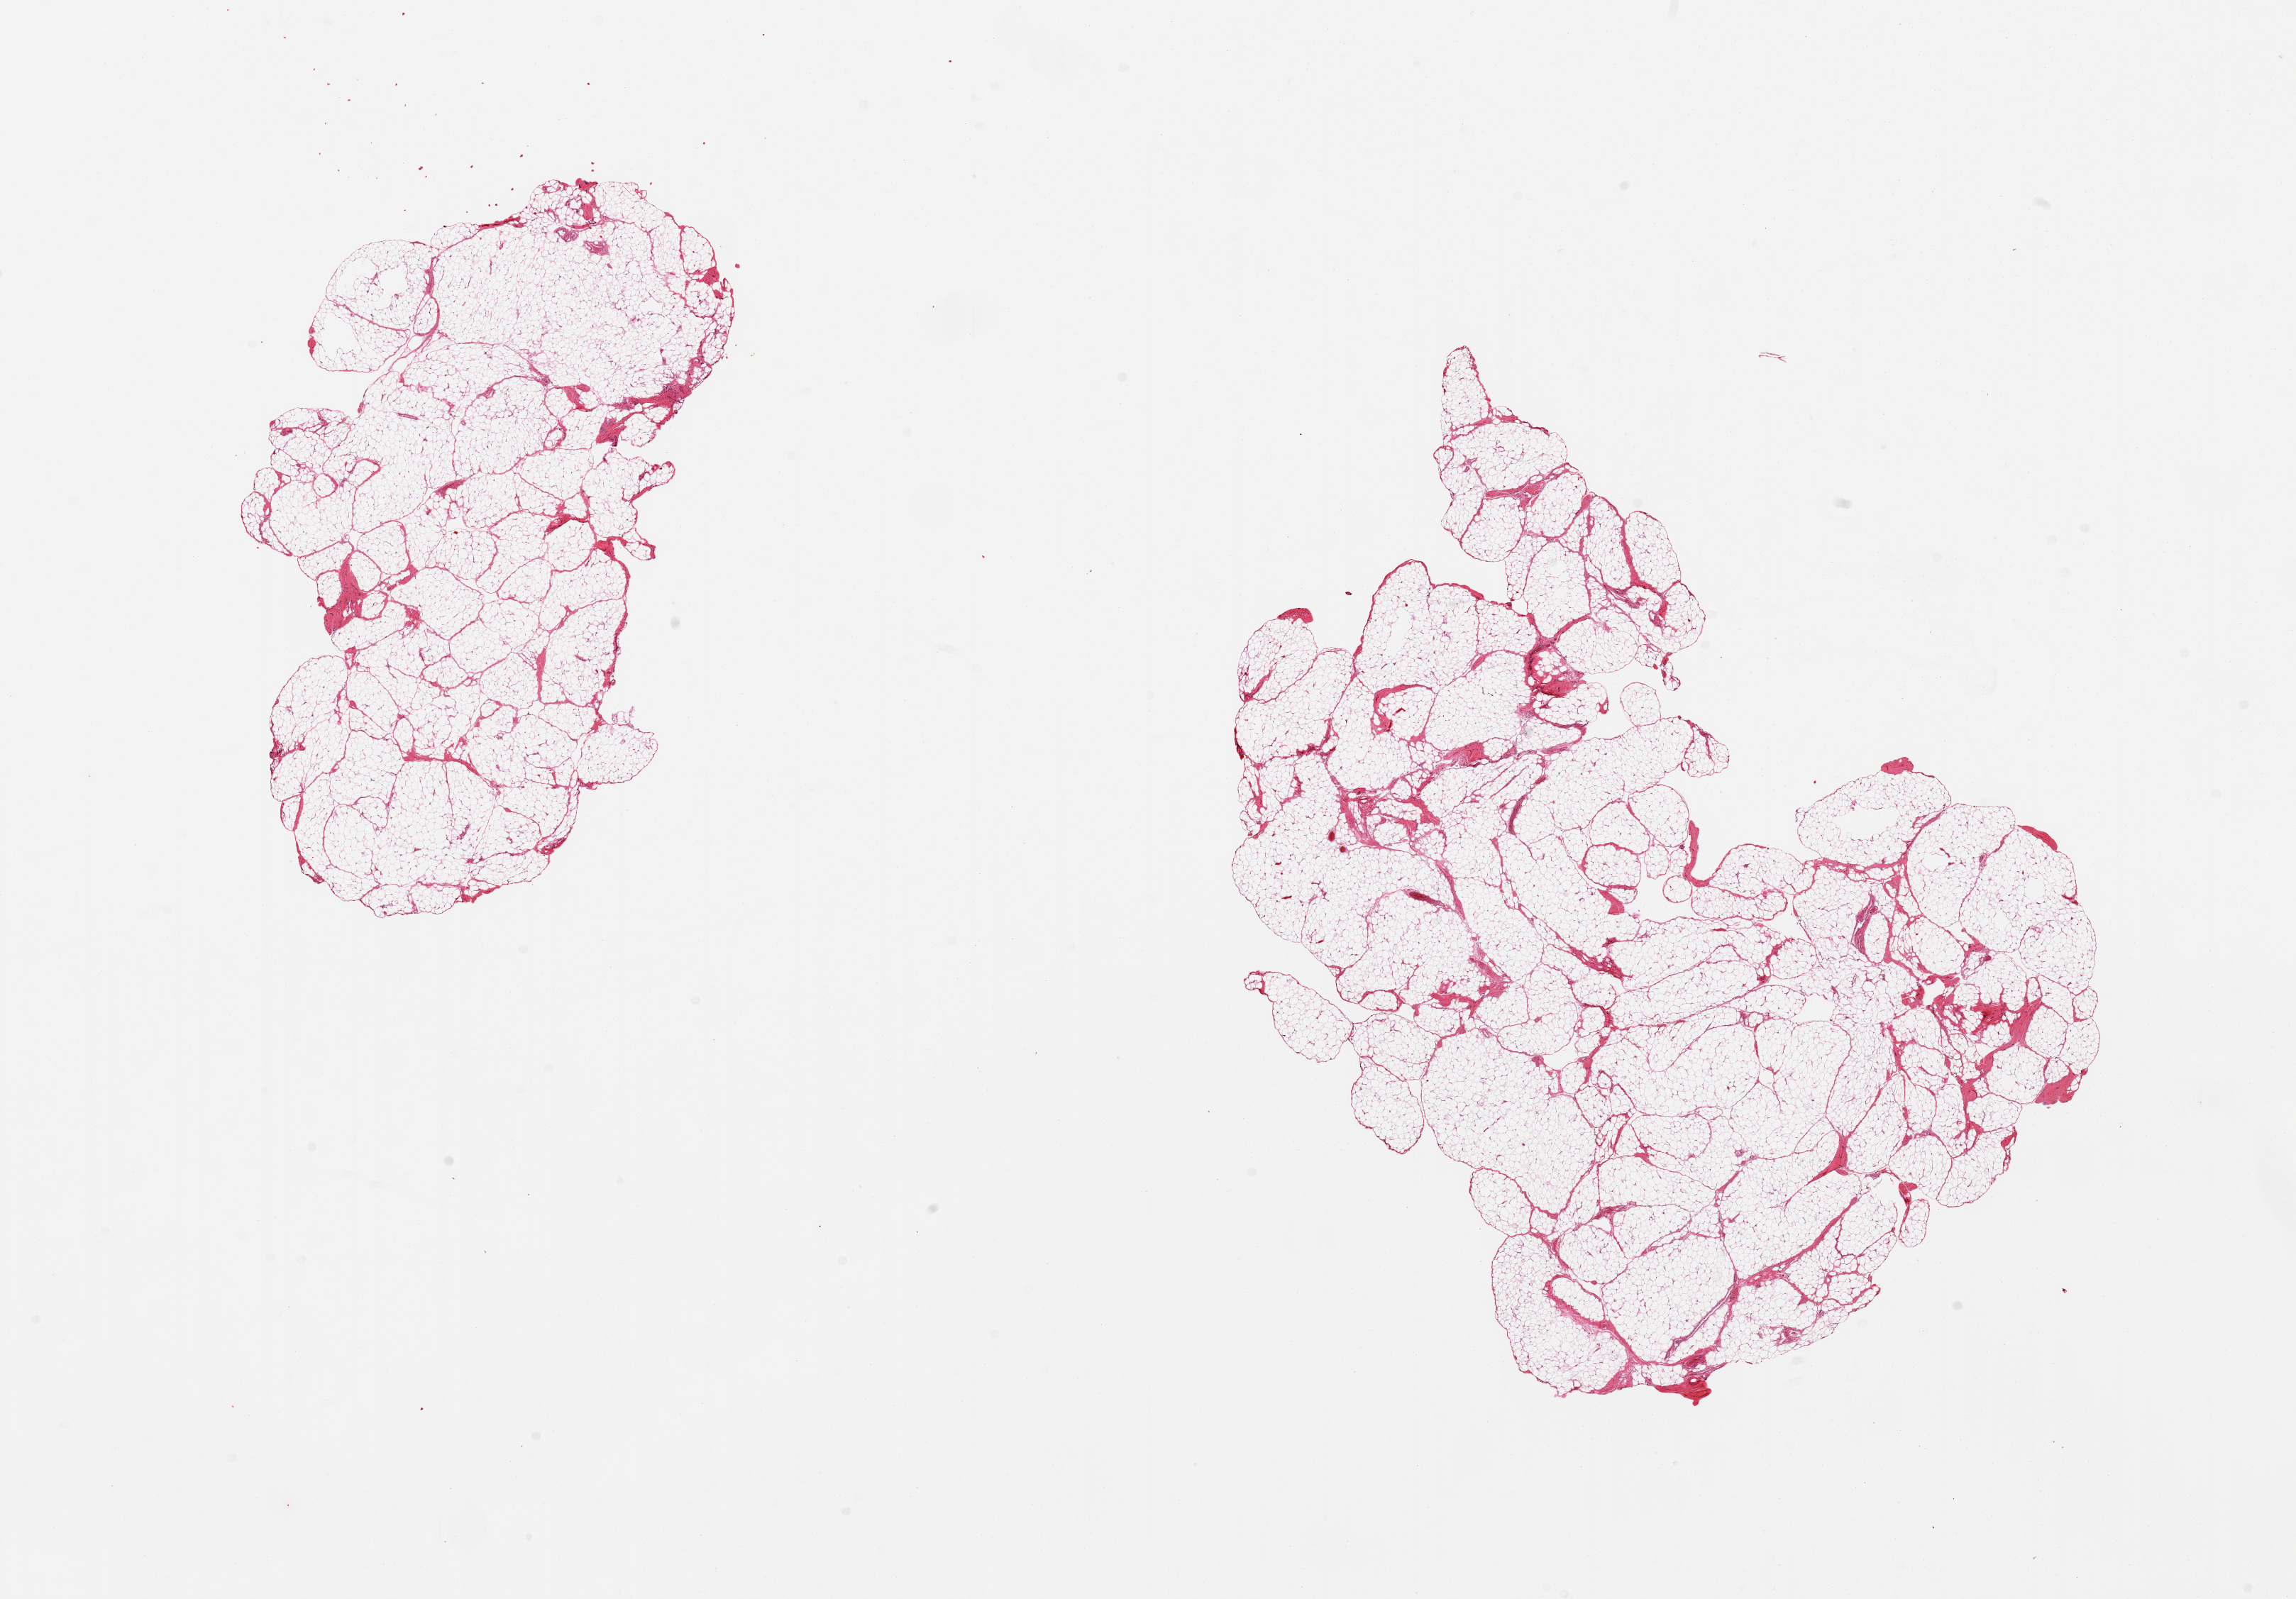
Hematoxylin and eosin (H&E) whole-slide image — low-resolution overview of the scanned area, about 25.6 x 17.8 mm (acquisition: 20x scan), PAXgene-fixed paraffin-embedded (PFPE) section, sampled site (target tissue): omentum, donor tissue sample. Donor sex: female.
- pathologist's review note for this sample: 2 pieces